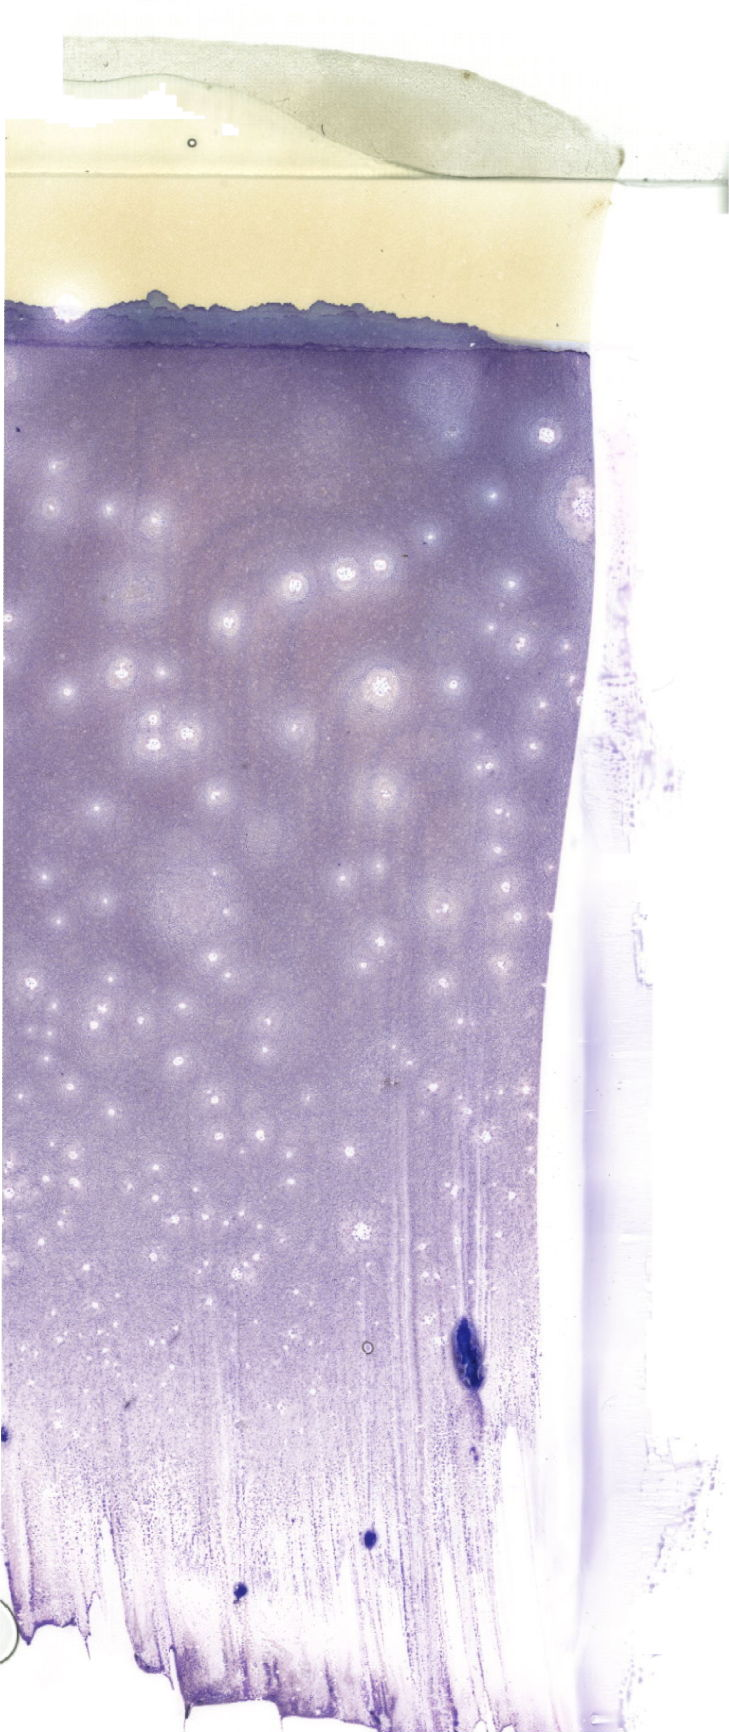
May-Grünwald-Giemsa (MGG)-stained marrow aspirate smear (whole slide), whole scanned area (about 20.7 x 49.1 mm) shown as a low-resolution overview. Patient sex: female.
- diagnosis: Acute Promyelocytic Leukemia with t(15;17)(q24.1;q21.2);PML-RARA